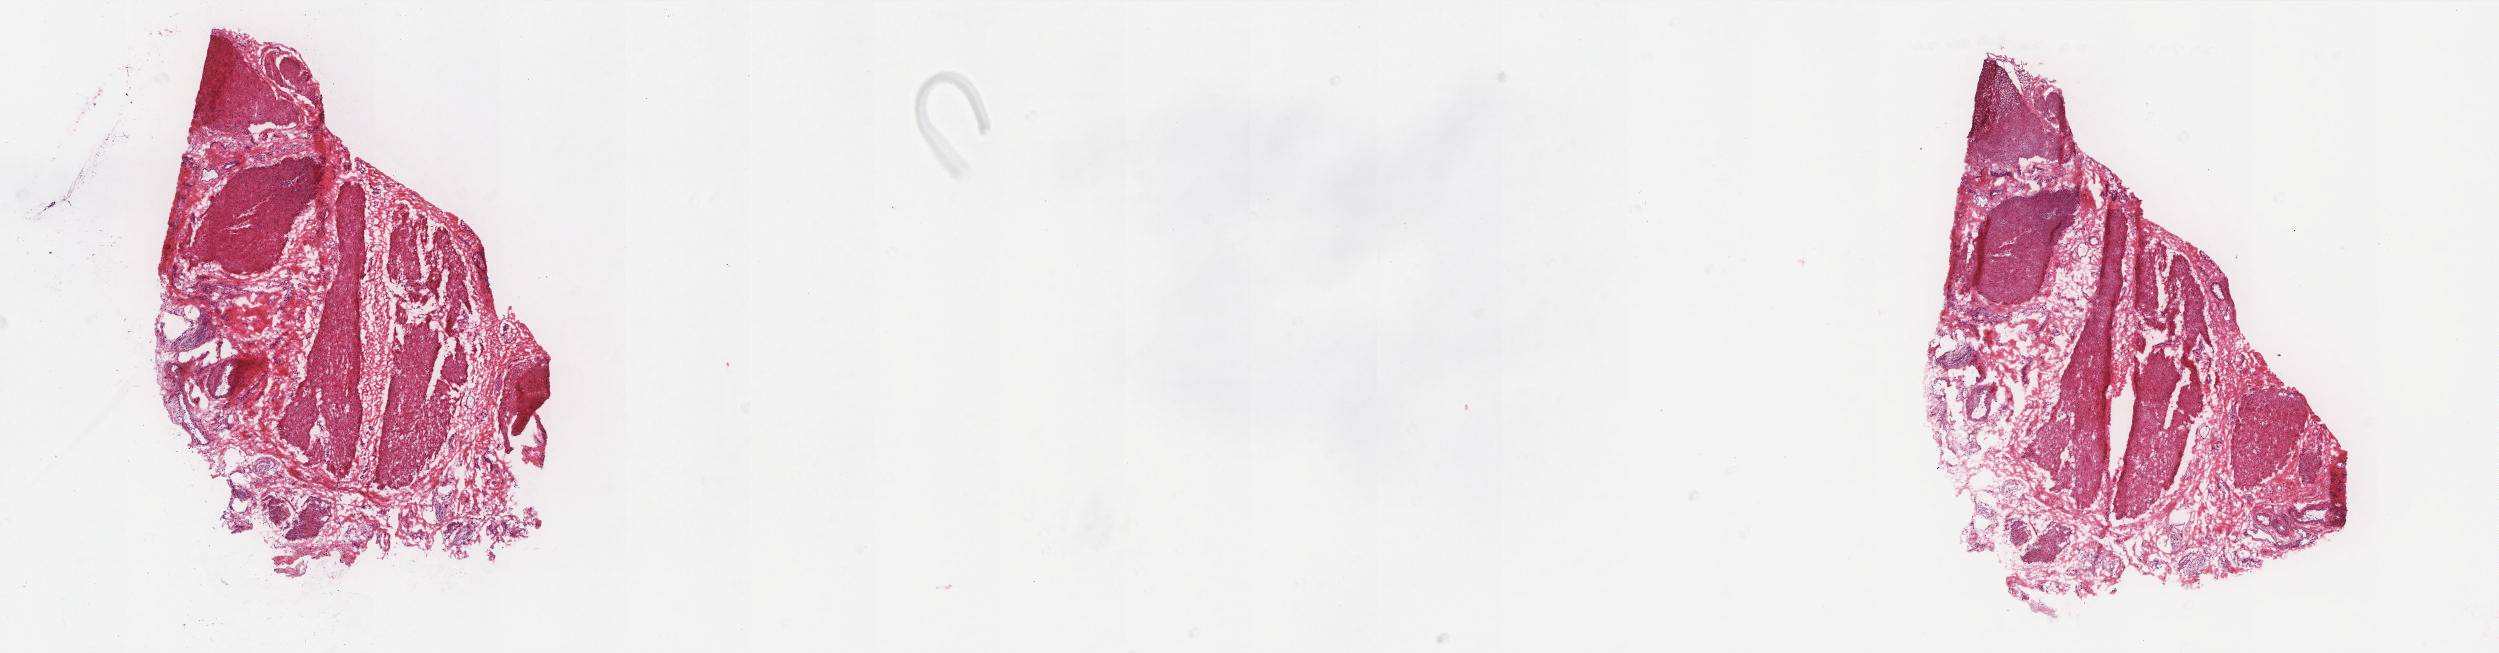
Digitized Hematoxylin and eosin (H&E) stained tissue section (whole slide) — low-resolution overview of the scanned area, about 20.0 x 5.2 mm. Frozen section from the top of the tissue portion. Solid tissue normal (non-tumour tissue) sample from the bladder. Male, age 83 years at initial diagnosis. Composition of this section per pathologist review: tumour cells 0%, tumour nuclei 0%, normal cells 100%, stromal cells 0%, necrosis 0%. Inflammatory infiltration, as recorded: lymphocyte infiltration 0%, monocyte infiltration 0%, neutrophil infiltration 0%.
This section: solid tissue normal sample (biorepository sample class). Patient diagnosis: Transitional cell carcinoma.